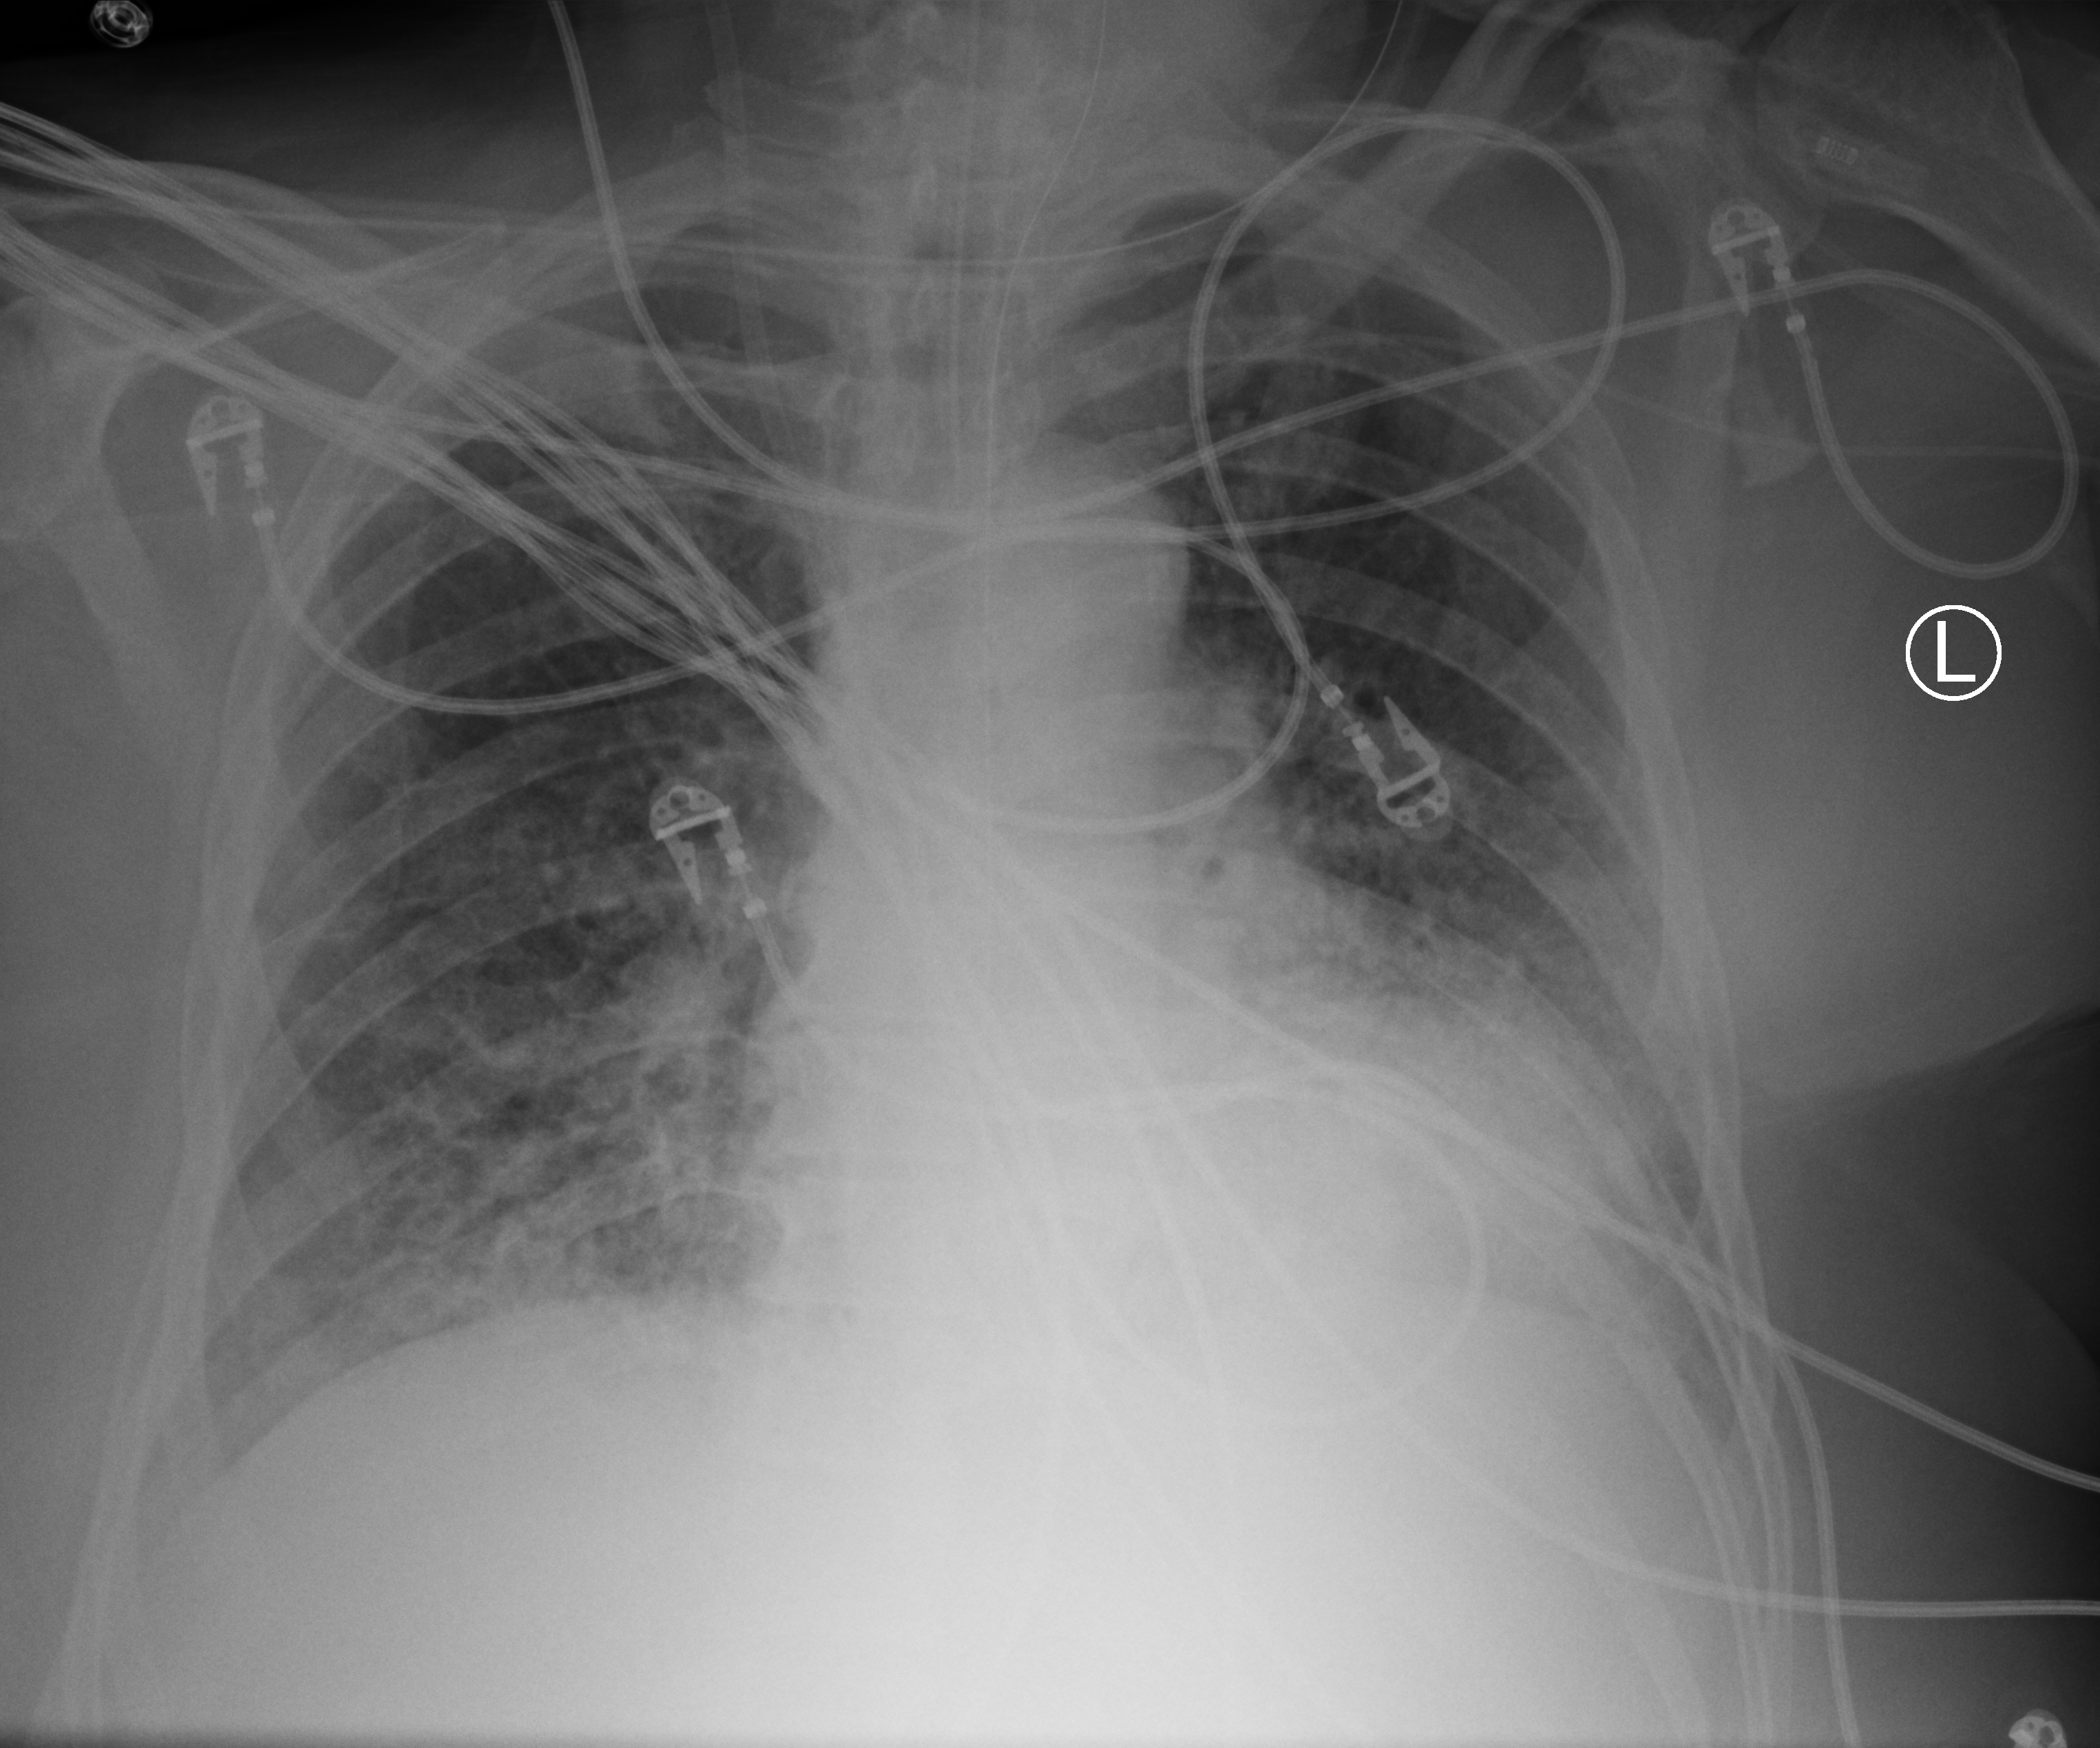
Chest X-ray (portable); anteroposterior (AP) projection. Patient hospitalised with COVID-19; male, aged 60–74 years.
Hospital-stay facts (about this admission, not read from this image; timing relative to this image not recorded):
- mechanically ventilated during this hospital stay: yes